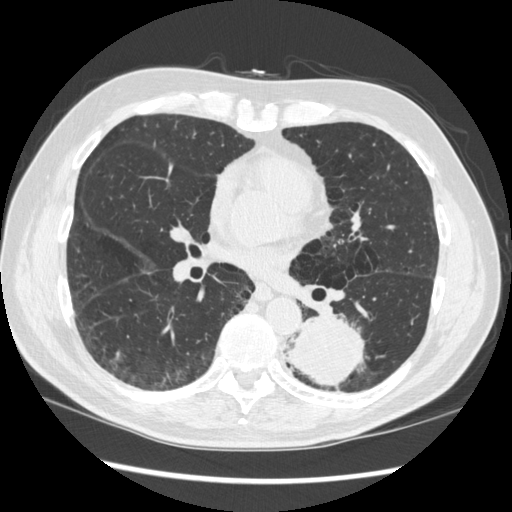
Chest CT (low-dose screening protocol), one axial image, first (baseline) screen, lung window (W 1500 / L -600 HU), 1.25 mm slice thickness, 512 × 512 image matrix. Male, age 72 years at enrolment.
Expert-annotated lung lesion, box from (x=266, y=304) to (x=370, y=396) px. The screening reader recorded 2 non-calcified nodules or masses ≥4 mm on this exam; which of them this box marks is not recorded. Participant outcome: lung cancer diagnosed 37 days after this screen — squamous cell carcinoma, NOS, left lower lobe, stage IIIA (AJCC 6th edition), 60 mm at pathology.